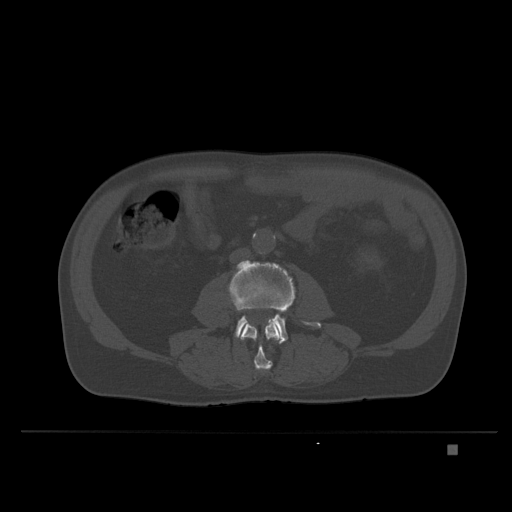
CT including the spine, one axial slice. Position 86 of 435 along the scan axis. Bone window (W 1800 / L 400 HU). 512 × 512 image matrix, field of view 434 × 434 mm. Patient: male, 73 years. From the clinical record (not read from this slice): primary cancer: skin.
Structures marked on this image (semi-automatically segmented with operator editing):
- L3 vertebra: bounding box <240,319,281,373> (left, top, right, bottom; pixels)
- L4 vertebra: <227,260,321,344>